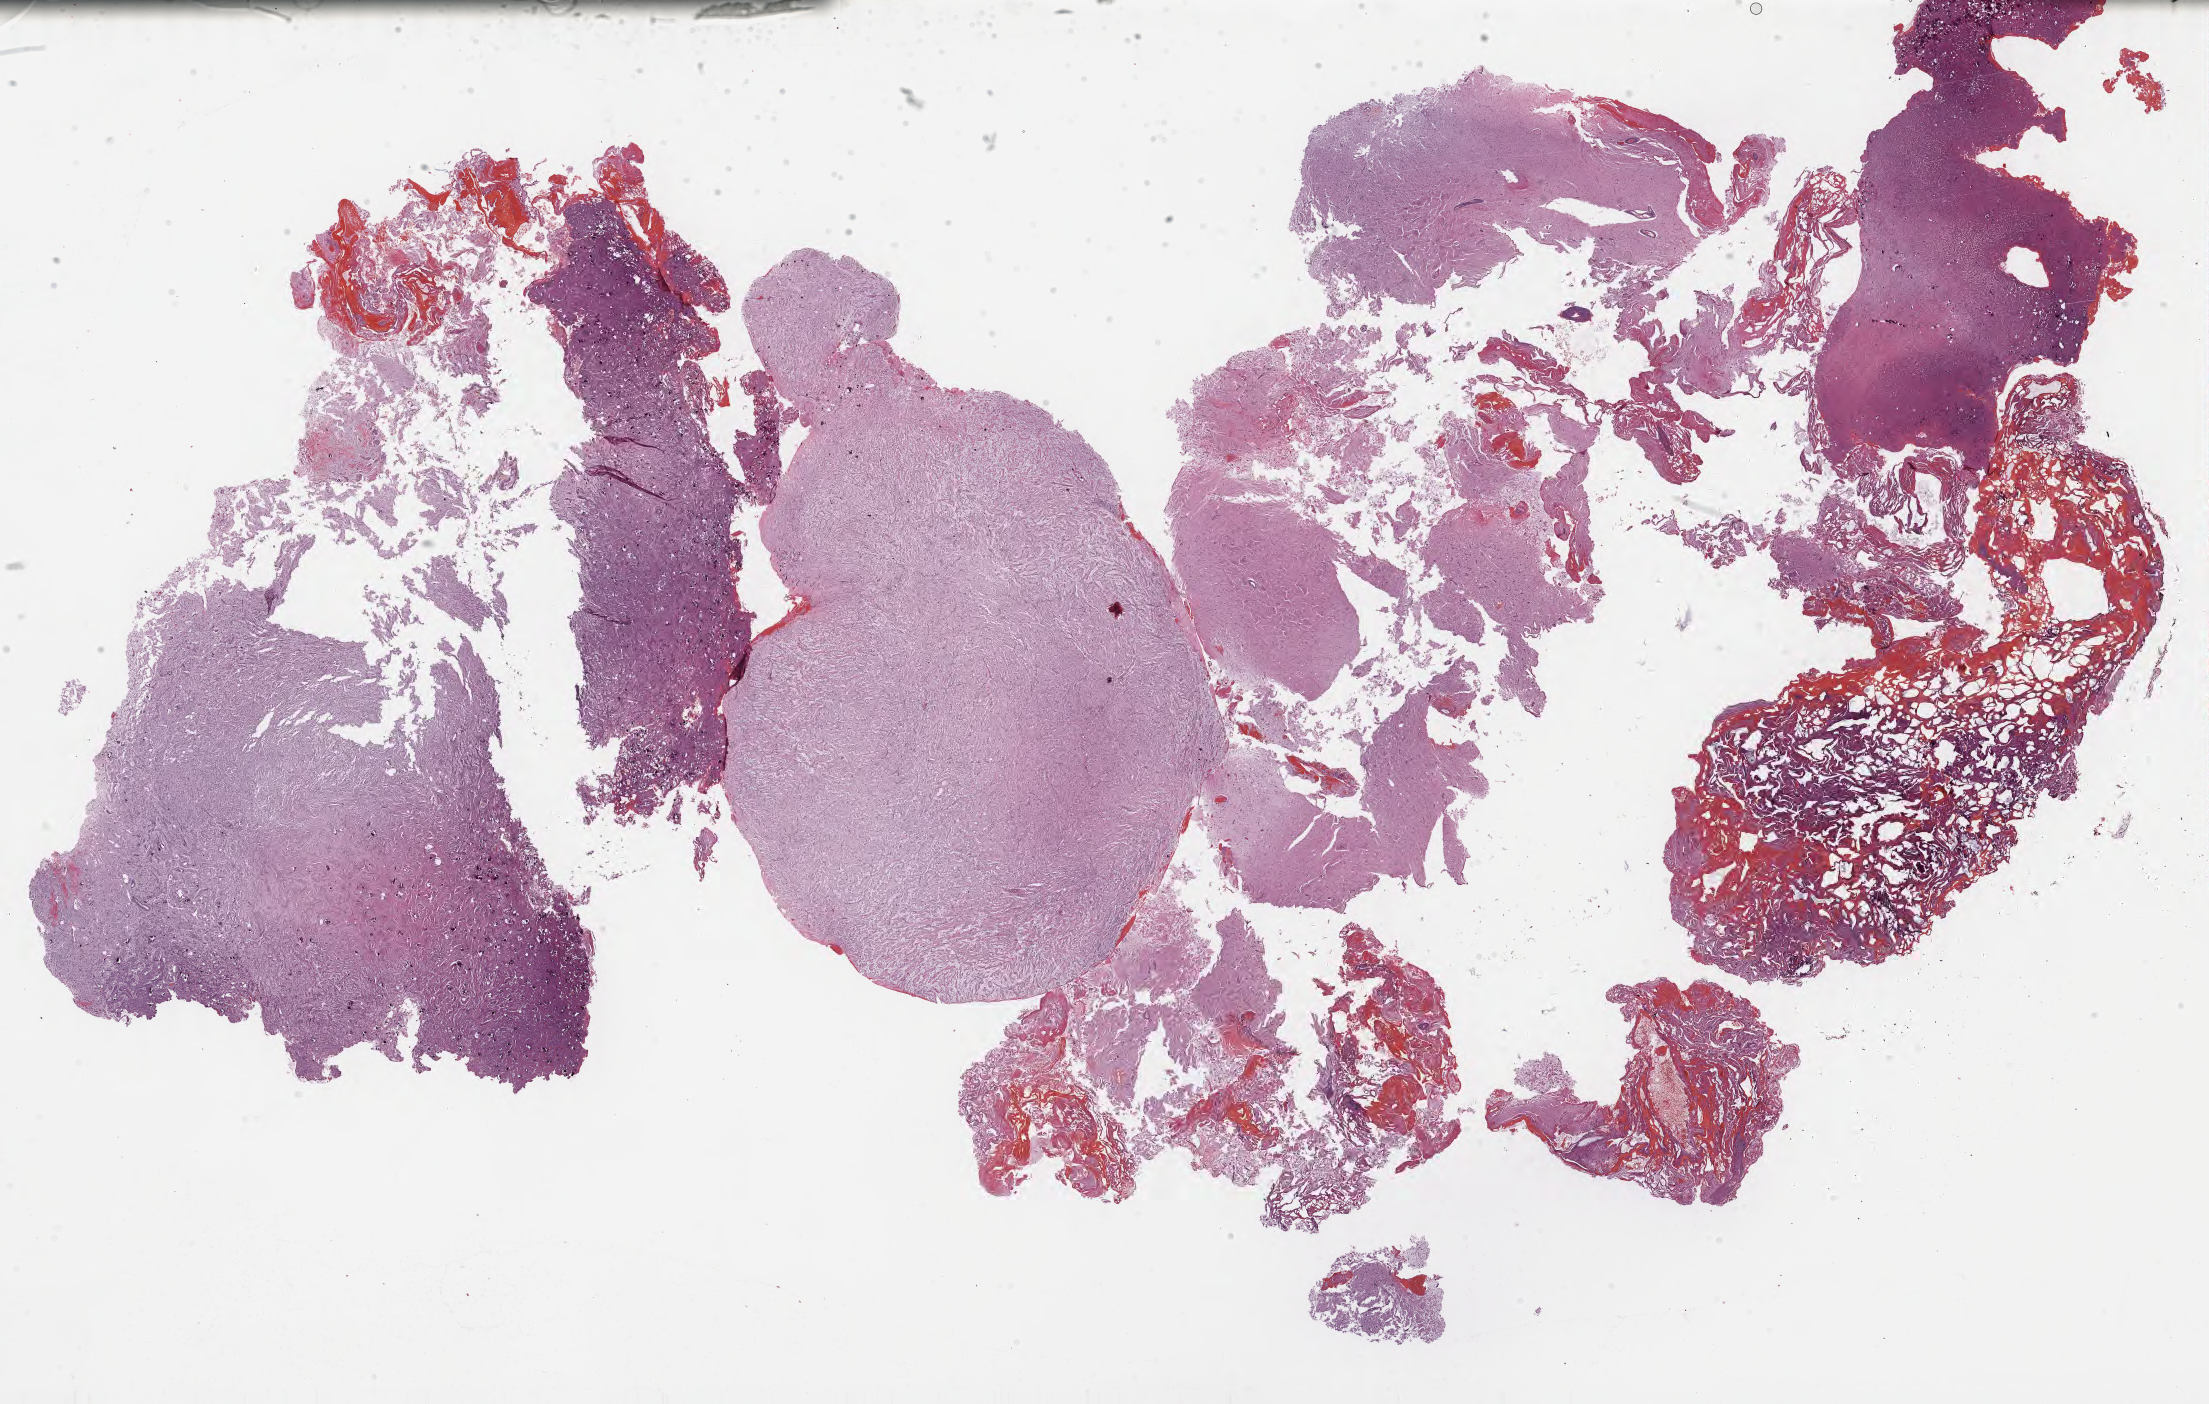
Haematoxylin and eosin whole-slide image of tumor tissue from the cerebral ventricle, a low-resolution overview of the entire scanned area, about 35.7 x 22.7 mm, formalin-fixed paraffin-embedded section. Patient: female, age 77 months (6 years 5 months).
Diagnosis (ICD-O-3 morphology term): Ganglioglioma, NOS.